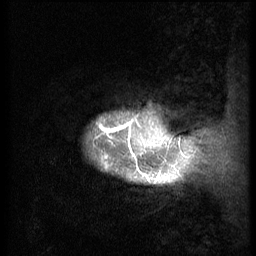
Breast MRI (dynamic contrast-enhanced), one sagittal slice; 3 images stored at this slice position (order not interpretable as contrast timing); 1.5 T; TE 4.2 ms, TR 9 ms; 2.5 mm slice thickness; 256 × 256 image matrix, field of view 180 × 180 mm. Patient: female, 49 years. Case-level facts recorded for this patient, not image findings: setting: breast cancer imaged before/during neoadjuvant chemotherapy; receptor status: HER2-positive.
Structures marked on this image (semi-automatically segmented with operator editing):
- analysis volume of interest (the breast-tissue region the enhancement analysis was run in; not a lesion): bounding box <70,89,168,206> (left, top, right, bottom; pixels)
- tumour enhancement mask (voxels above the 140 % enhancement threshold inside the analysis volume of interest): <99,124,135,157>